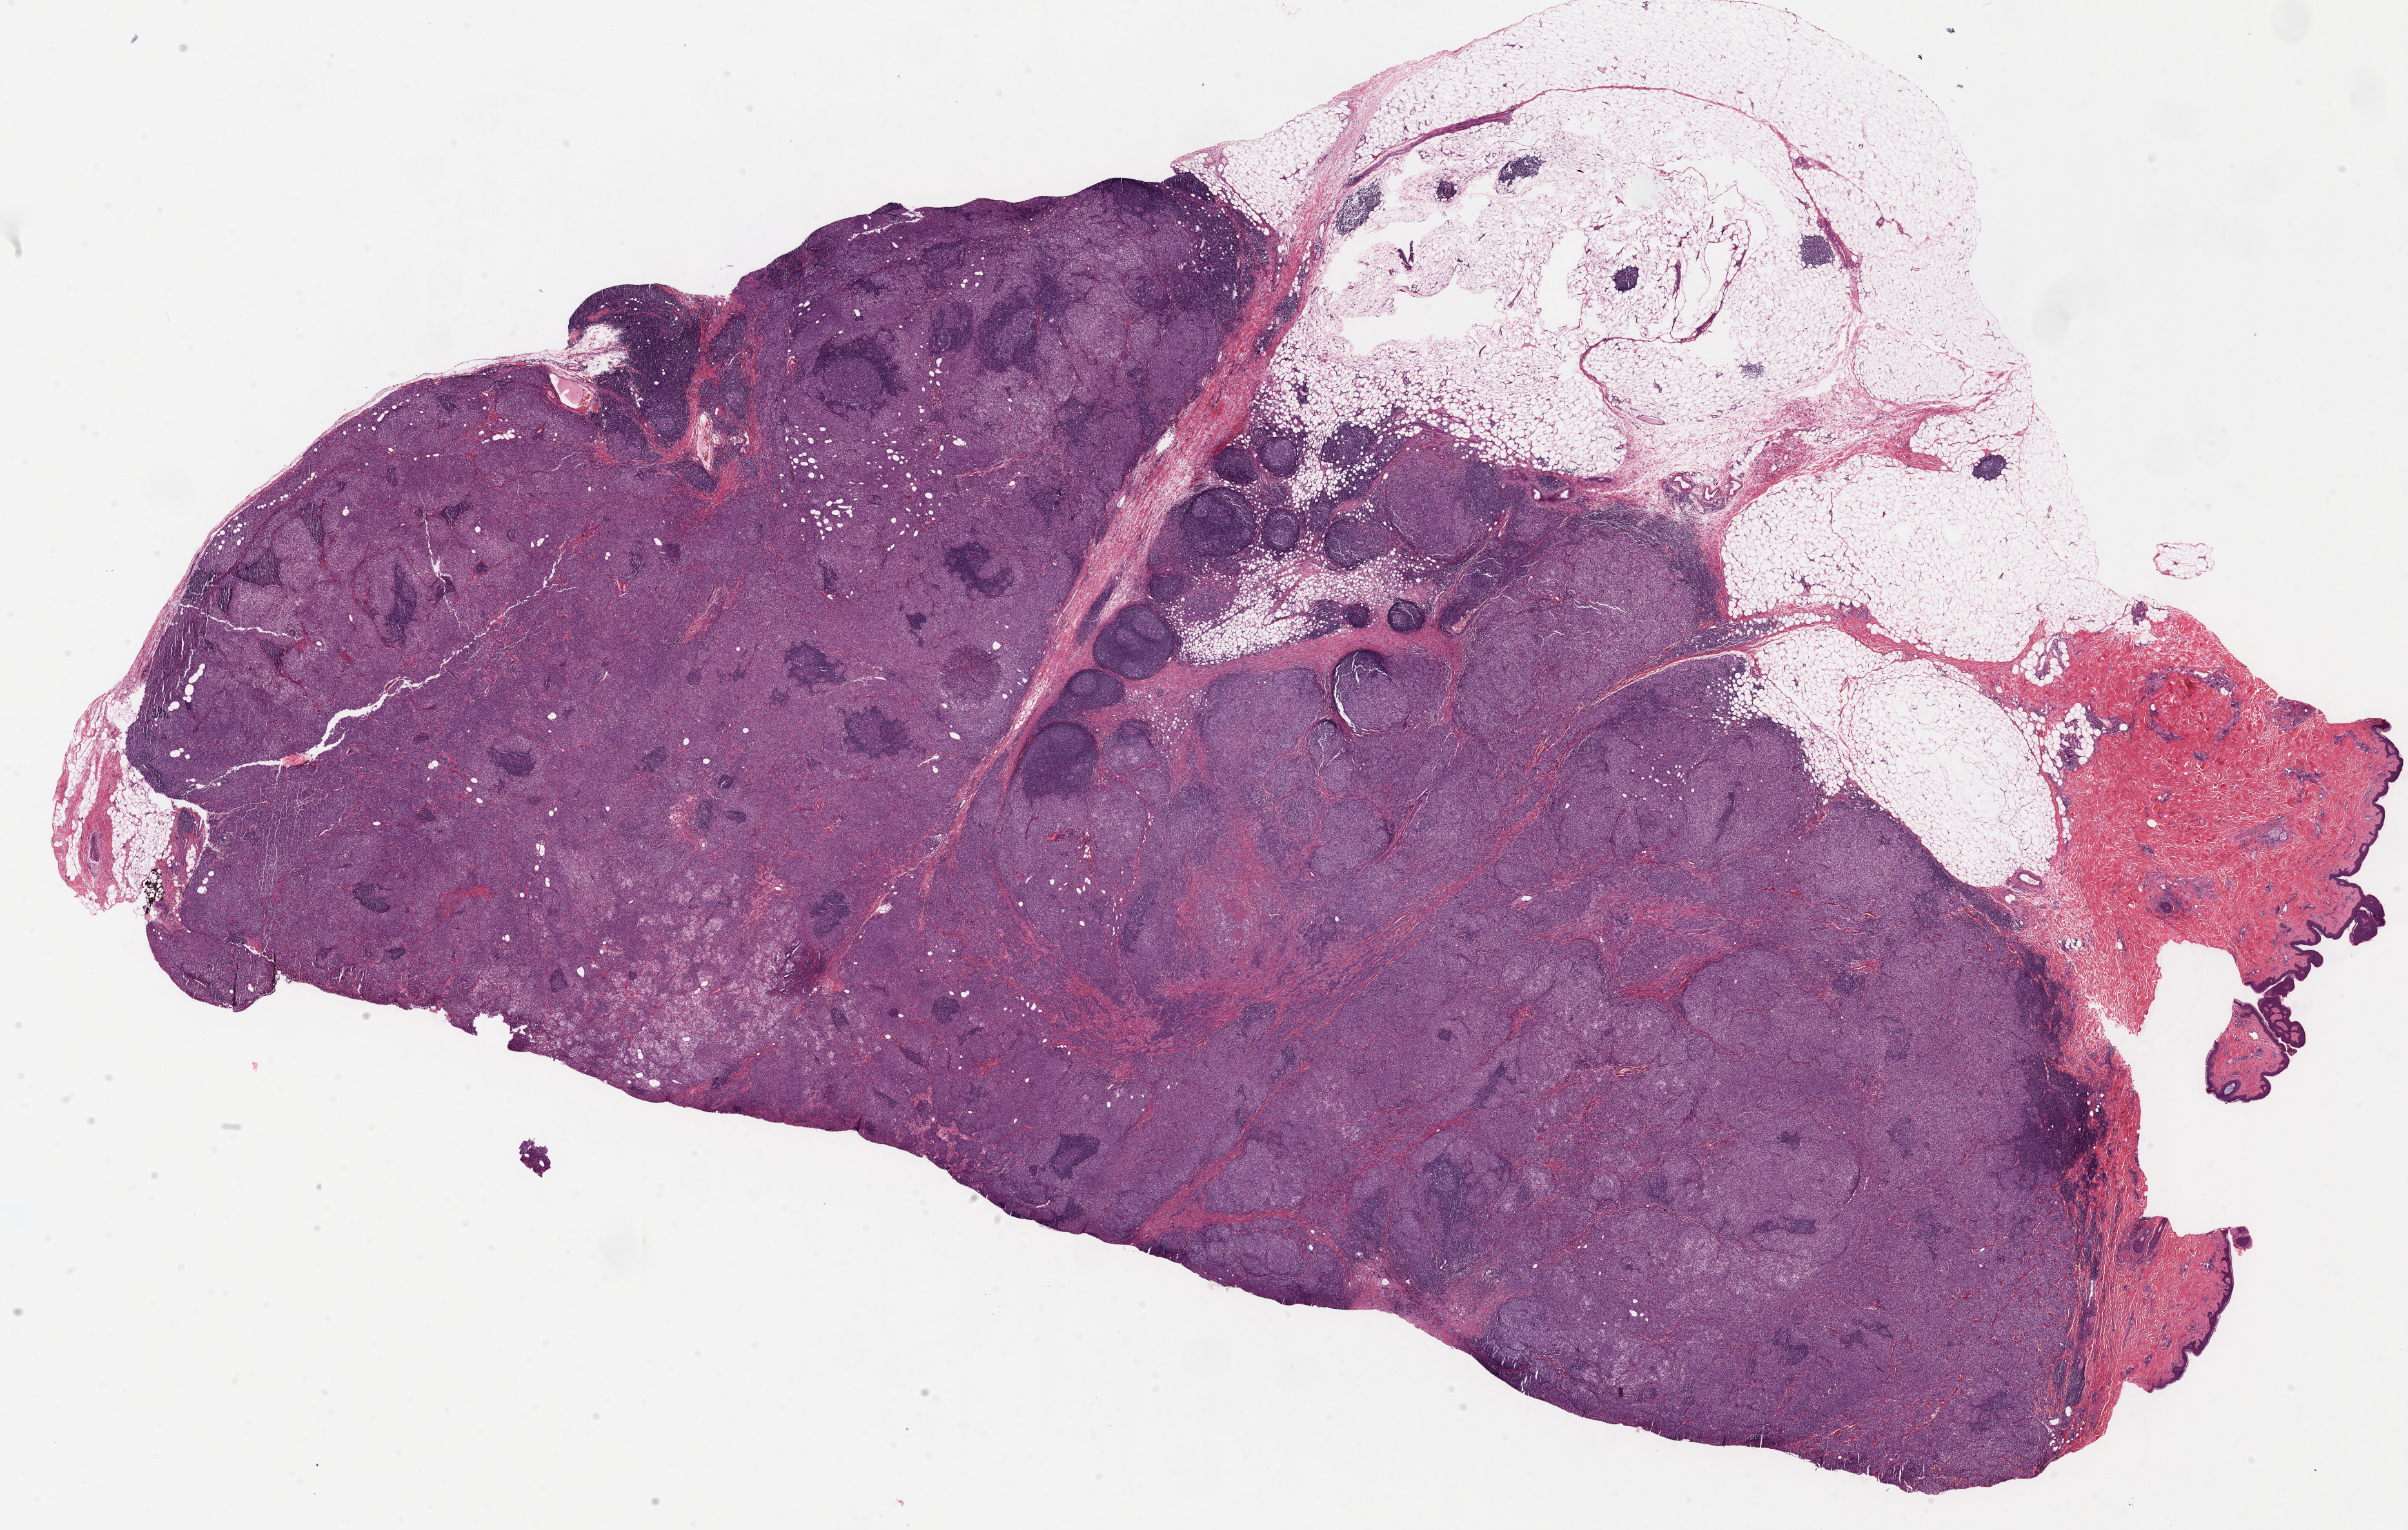
Digitized Hematoxylin and eosin (H&E) stained tissue section (whole slide), shown as a low-resolution overview of the whole scanned area (about 29.8 x 19.0 mm); formalin-fixed paraffin-embedded (FFPE) diagnostic section; primary tumour sample from the breast. Female, age 64 years at initial diagnosis.
• TNM: T2 N0 (i-) M0
• AJCC pathologic stage: IIA
• diagnosis: Infiltrating duct carcinoma, NOS
• laterality: right